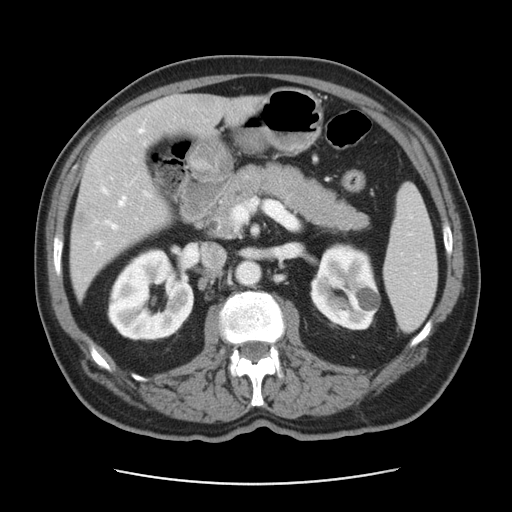
Contrast-enhanced abdominal CT, one axial slice. Slice 21 of 42 in the series (ordered by position). Reconstruction kernel STANDARD. 120 kVp. Soft-tissue window (W 400 / L 40 HU). 5 mm slice thickness. 512 × 512 image matrix, field of view 370 × 370 mm. Male patient, age 73 years. Case-level facts recorded for this patient, not image findings: diagnosis: colorectal cancer liver metastases, imaged before liver resection; multiple liver metastases: yes; largest metastasis: 0.5 cm; disease in both lobes: no.
Structures marked on this image (outlined manually by an expert reader):
- hepatic veins: bounding box (x1, y1, x2, y2) in pixels: (95, 130, 143, 248)
- liver: (73, 96, 255, 297)
- planned liver remnant (the part of the liver to remain after resection): (111, 96, 255, 164)
- portal vein (with intrahepatic branches): (109, 192, 150, 229)
- liver metastasis: (77, 212, 84, 223)